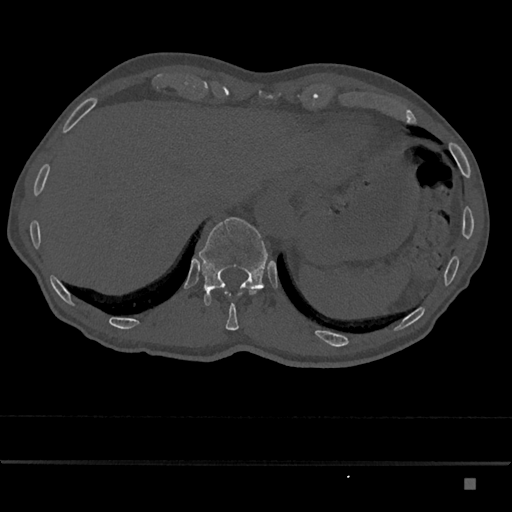
CT including the spine, one axial slice. Position 640 of 797 along the scan axis. Reconstruction kernel Br40s/3. Bone window (W 1800 / L 400 HU). 0.5 mm slice thickness. 512 × 512 image matrix, field of view 390 × 390 mm. Patient: male, 72 years. Case-level facts recorded for this patient, not image findings: primary cancer: prostate.
Structures marked on this image (semi-automatically segmented with operator editing):
- T11 vertebra: box from (x=226, y=290) to (x=256, y=330) px
- T12 vertebra: (x=199, y=217)–(x=268, y=306)